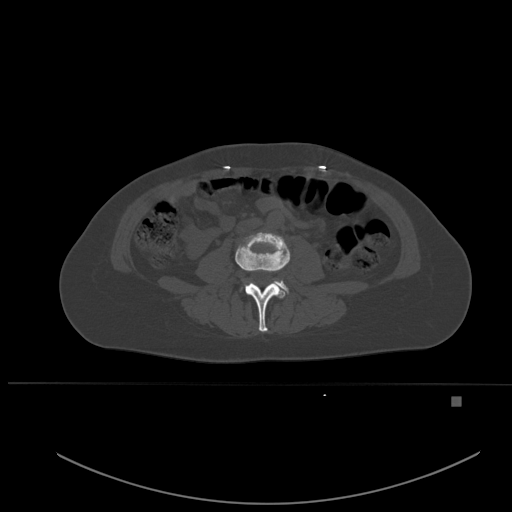
CT including the spine, one axial slice; slice 187 of 651 in the series (ordered by position); bone window (W 1800 / L 400 HU); 512 × 512 image matrix. Patient: female, 49 years. Case-level facts recorded for this patient, not image findings: primary cancer: breast.
Outlined on this slice (semi-automatically segmented with operator editing):
- L3 vertebra: box from (x=235, y=232) to (x=290, y=332) px
- L4 vertebra: (x=244, y=280)–(x=289, y=293)